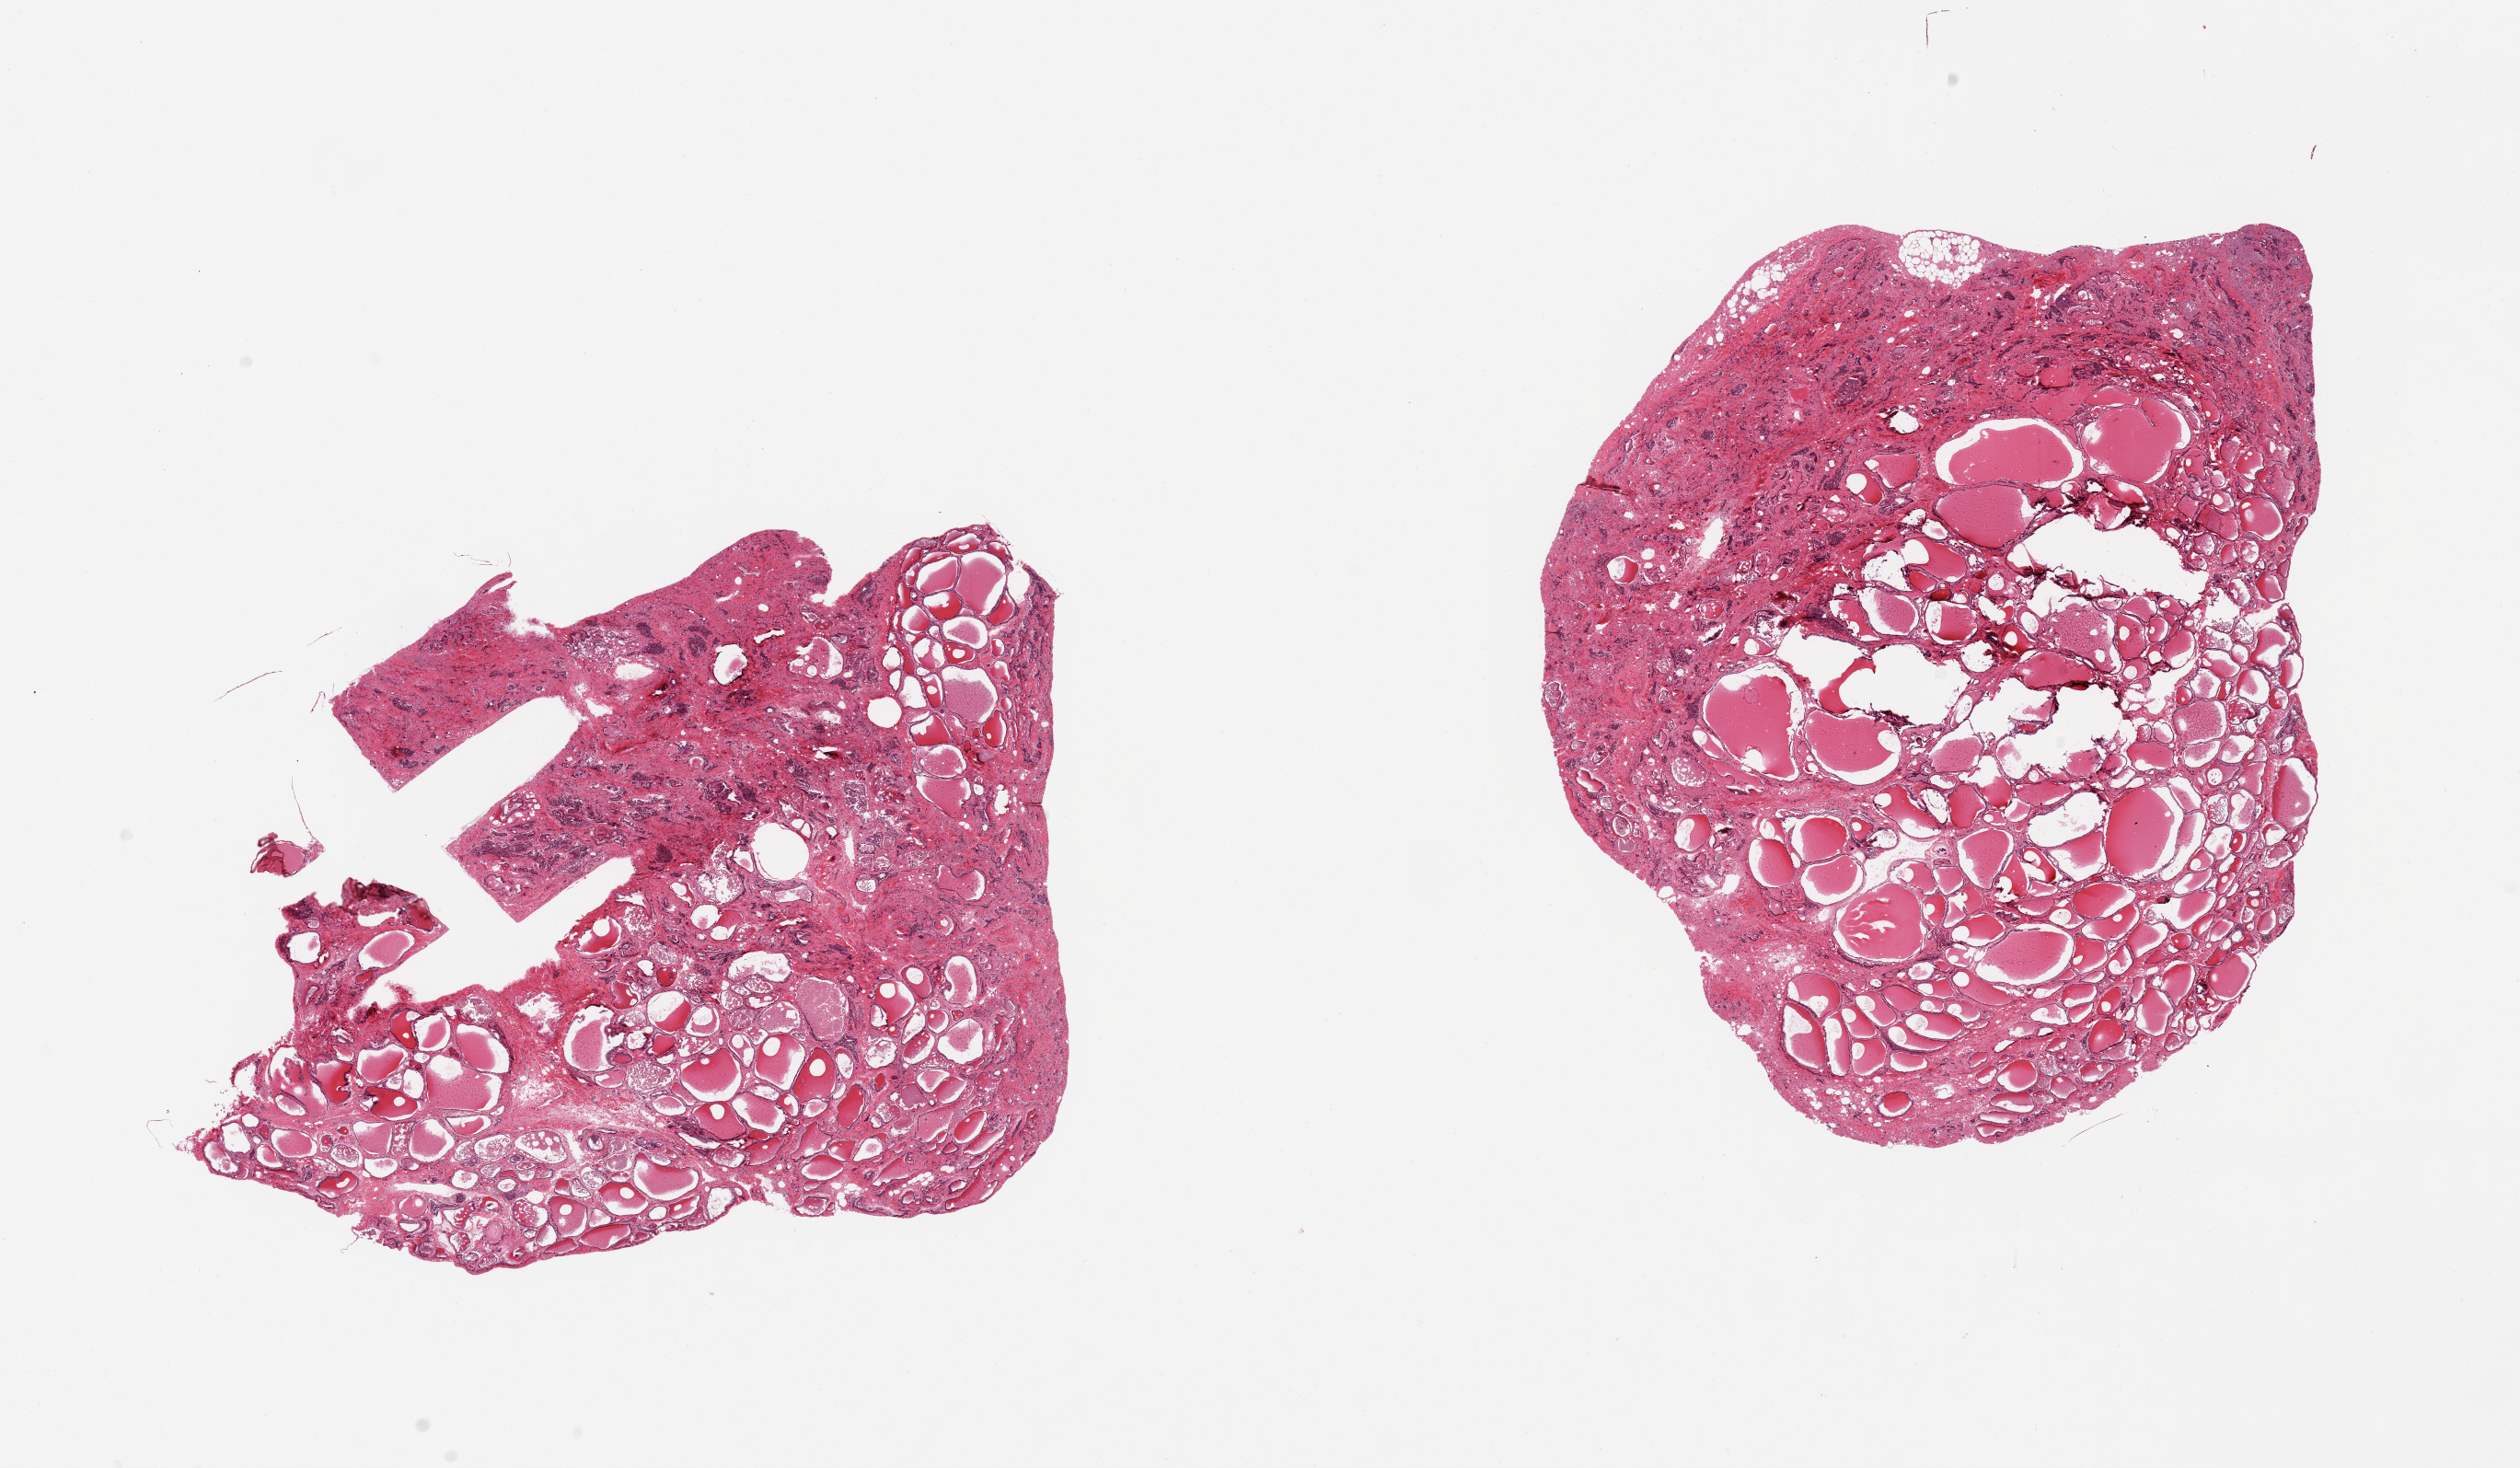
Digitized hematoxylin and eosin (H&E)-stained section — whole scanned area (about 21.7 x 12.6 mm) shown as a low-resolution overview; PAXgene-fixed, paraffin-embedded tissue; sampled site (target tissue): thyroid; donor tissue sample. Donor: male.
Review note (as recorded): 2 pieces; fibrosis represents about 30% of tissue; variably sized thyroid follicles.